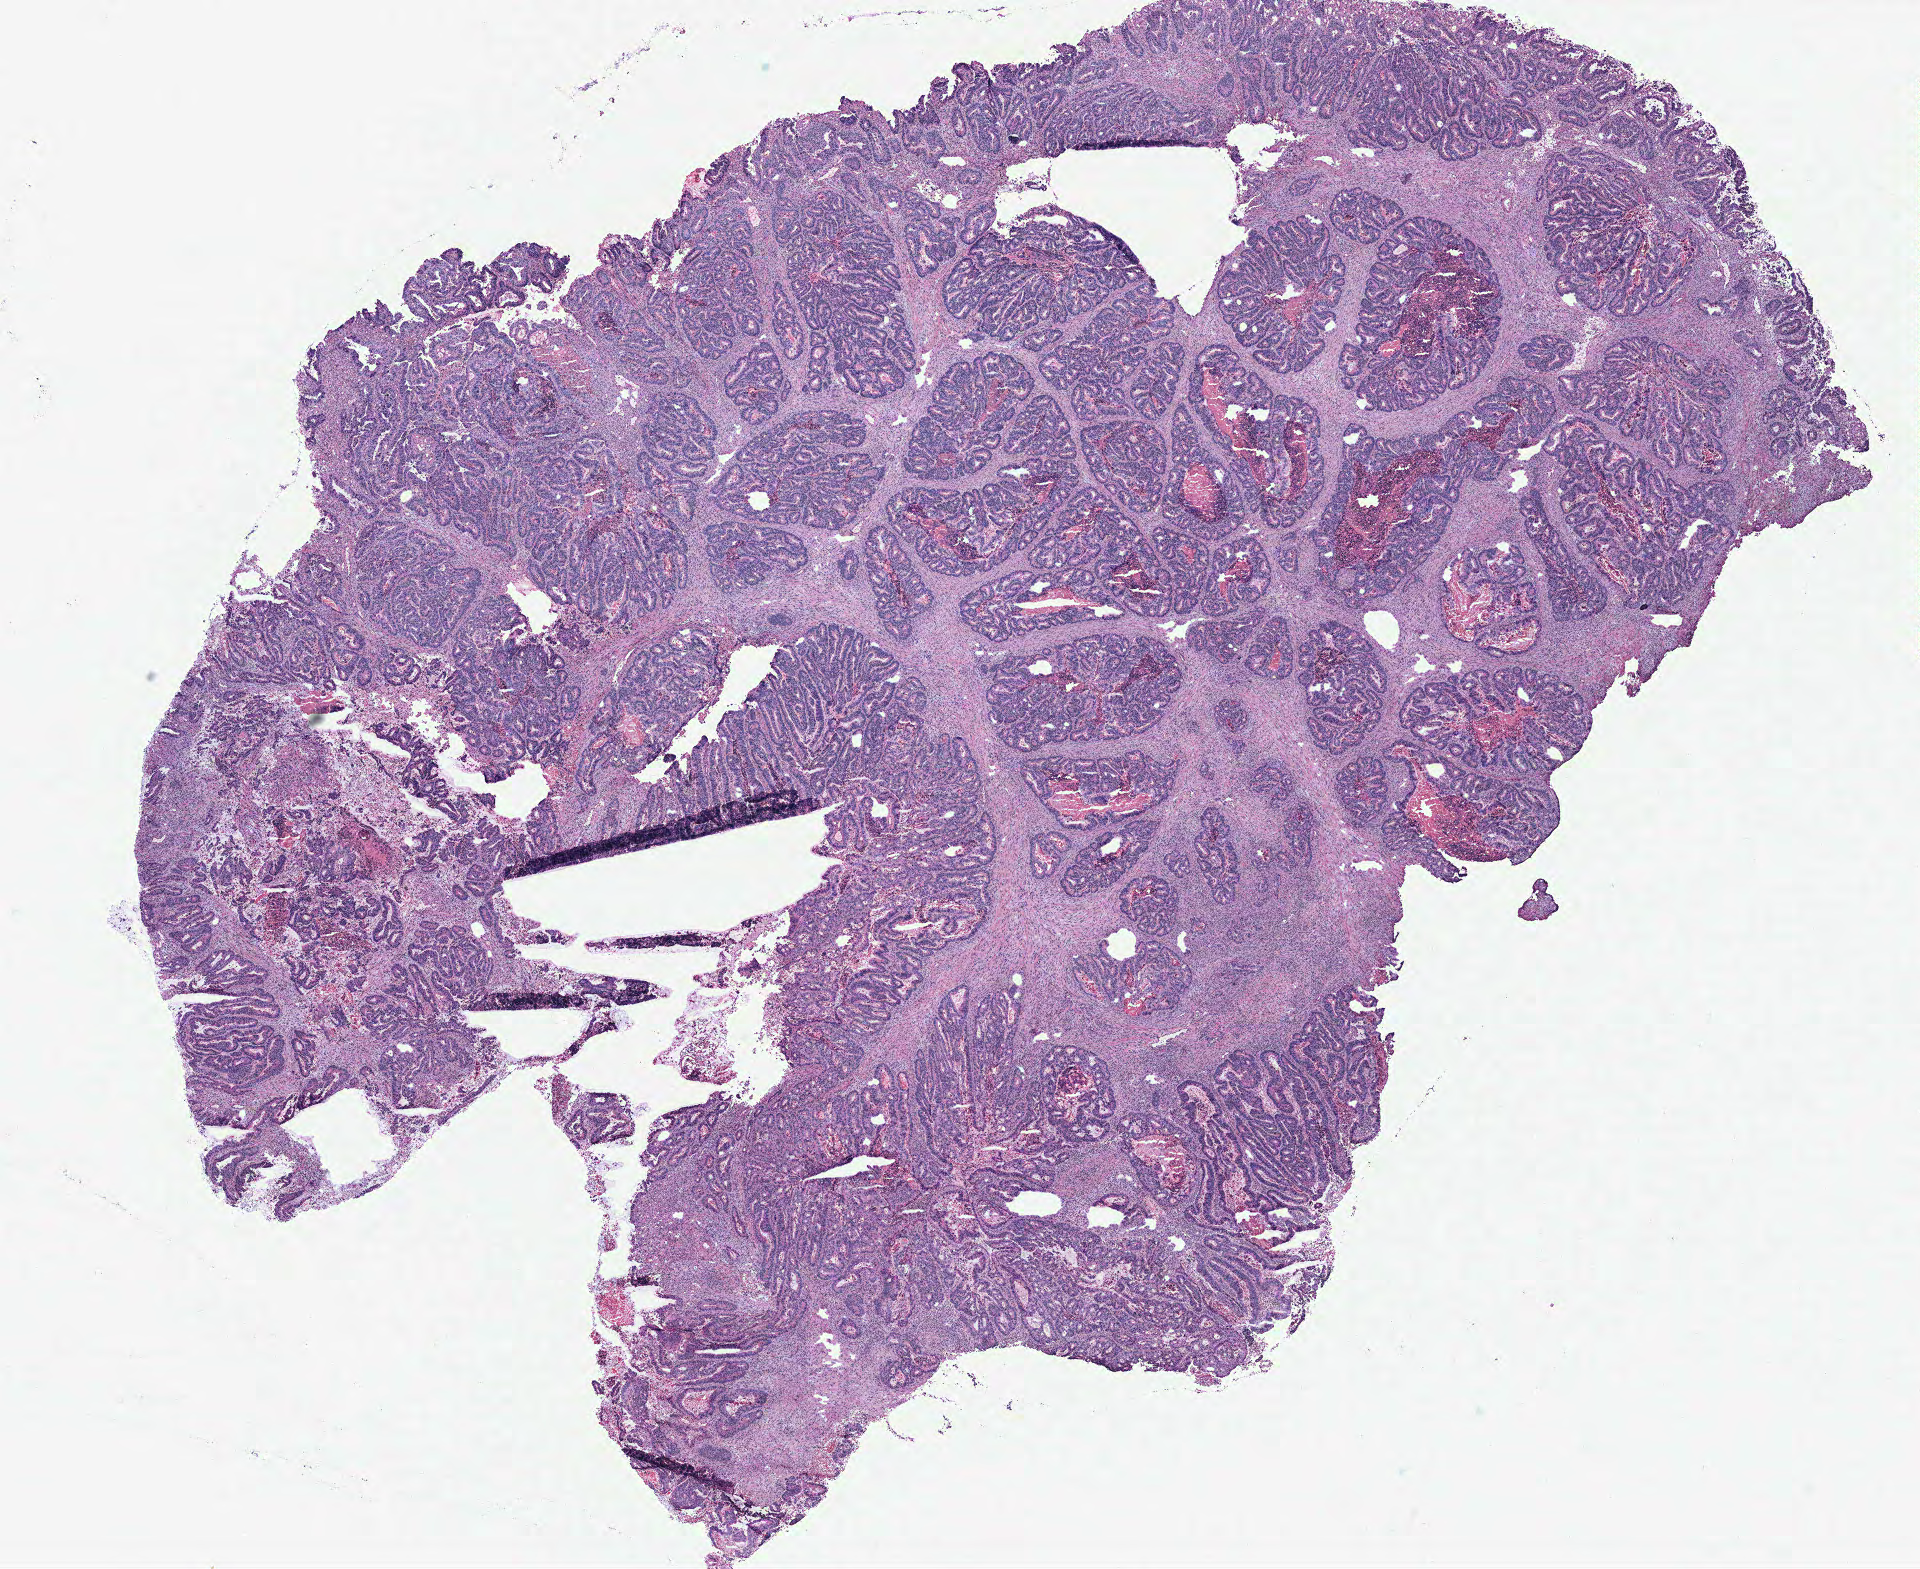
Hematoxylin and eosin (H&E) stained whole-slide image, shown as a low-resolution overview of the whole scanned area (about 15.4 x 12.6 mm, acquisition: 40x scan), normal (non-tumour) tissue sample, colon. Patient: male, age 88 years.
This section: normal (non-tumour) tissue from the same patient. Patient diagnosis: Adenocarcinoma, NOS.